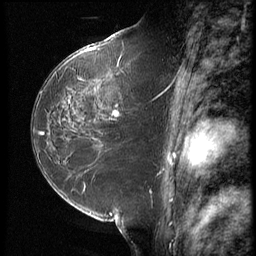
Breast MRI (dynamic contrast-enhanced), one sagittal slice. Position 36 of 64 along the scan axis. 3 images stored at this slice position (order not interpretable as contrast timing). 1.5 T. TE 4.2 ms, TR 9 ms. 2.5 mm slice thickness. 256 × 256 image matrix, field of view 180 × 180 mm. Patient: female, 59 years. From the clinical record (not read from this slice): setting: breast cancer imaged before/during neoadjuvant chemotherapy; receptor status: HER2-positive.
Annotated regions visible in this slice (semi-automatically segmented with operator editing):
- analysis volume of interest (the breast-tissue region the enhancement analysis was run in; not a lesion): bounding box (x1, y1, x2, y2) in pixels: (54, 65, 155, 132)
- tumour enhancement mask (voxels above the 140 % enhancement threshold inside the analysis volume of interest): (113, 110, 119, 116)